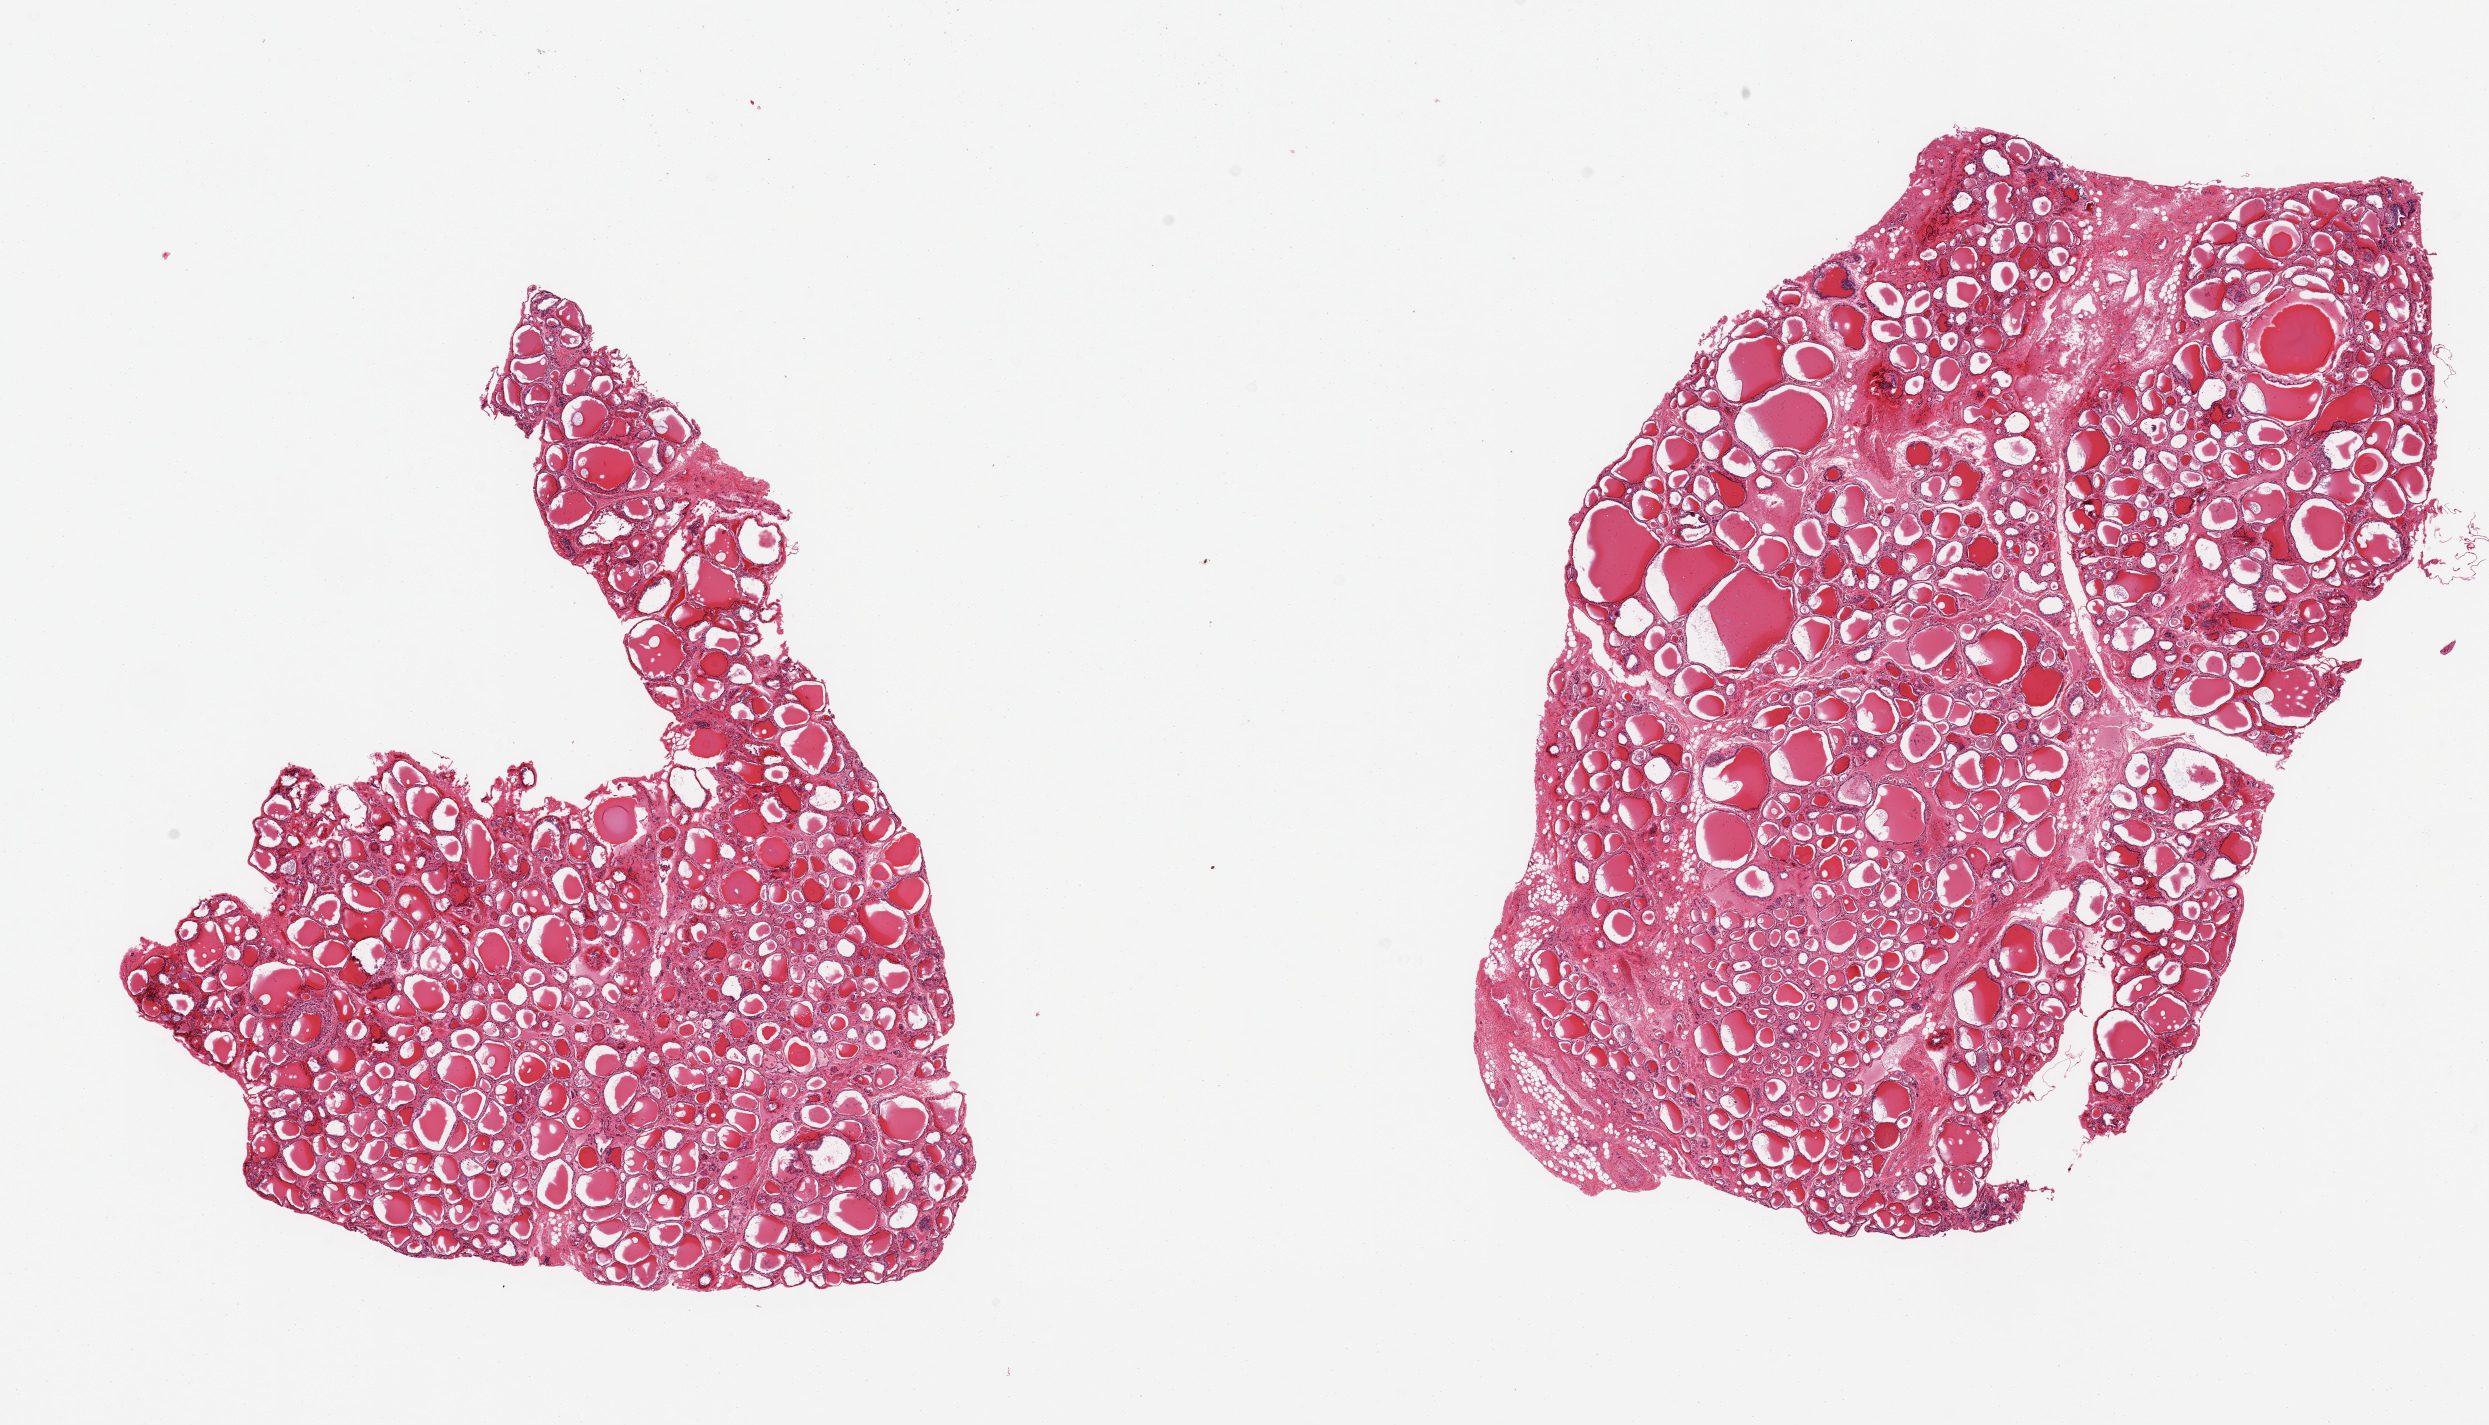
Whole-slide image, haematoxylin and eosin stain — shown as a low-resolution overview of the whole scanned area (about 19.7 x 11.3 mm, from a 20x scan), PAXgene-fixed paraffin-embedded (PFPE) section, section of thyroid (target tissue), tissue donor sample. Donor sex: male.
Reviewer comment on this tissue sample: 2 pieces; 5% fibrofatty content.